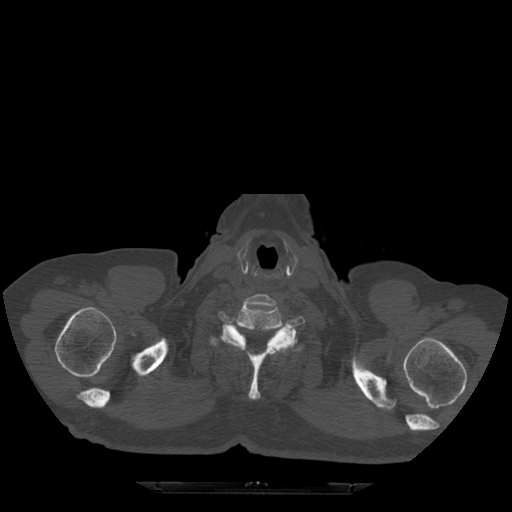
CT including the spine, one axial slice; position 449 of 522 along the scan axis; bone window (W 1800 / L 400 HU); 1.25 mm slice thickness; 512 × 512 image matrix. Patient age 72 years. From the clinical record (not read from this slice): primary cancer: prostate.
Outlined on this slice (semi-automatic segmentation, software-assisted and operator-edited):
- T1 vertebra: bounding box <209,326,305,400> (left, top, right, bottom; pixels)